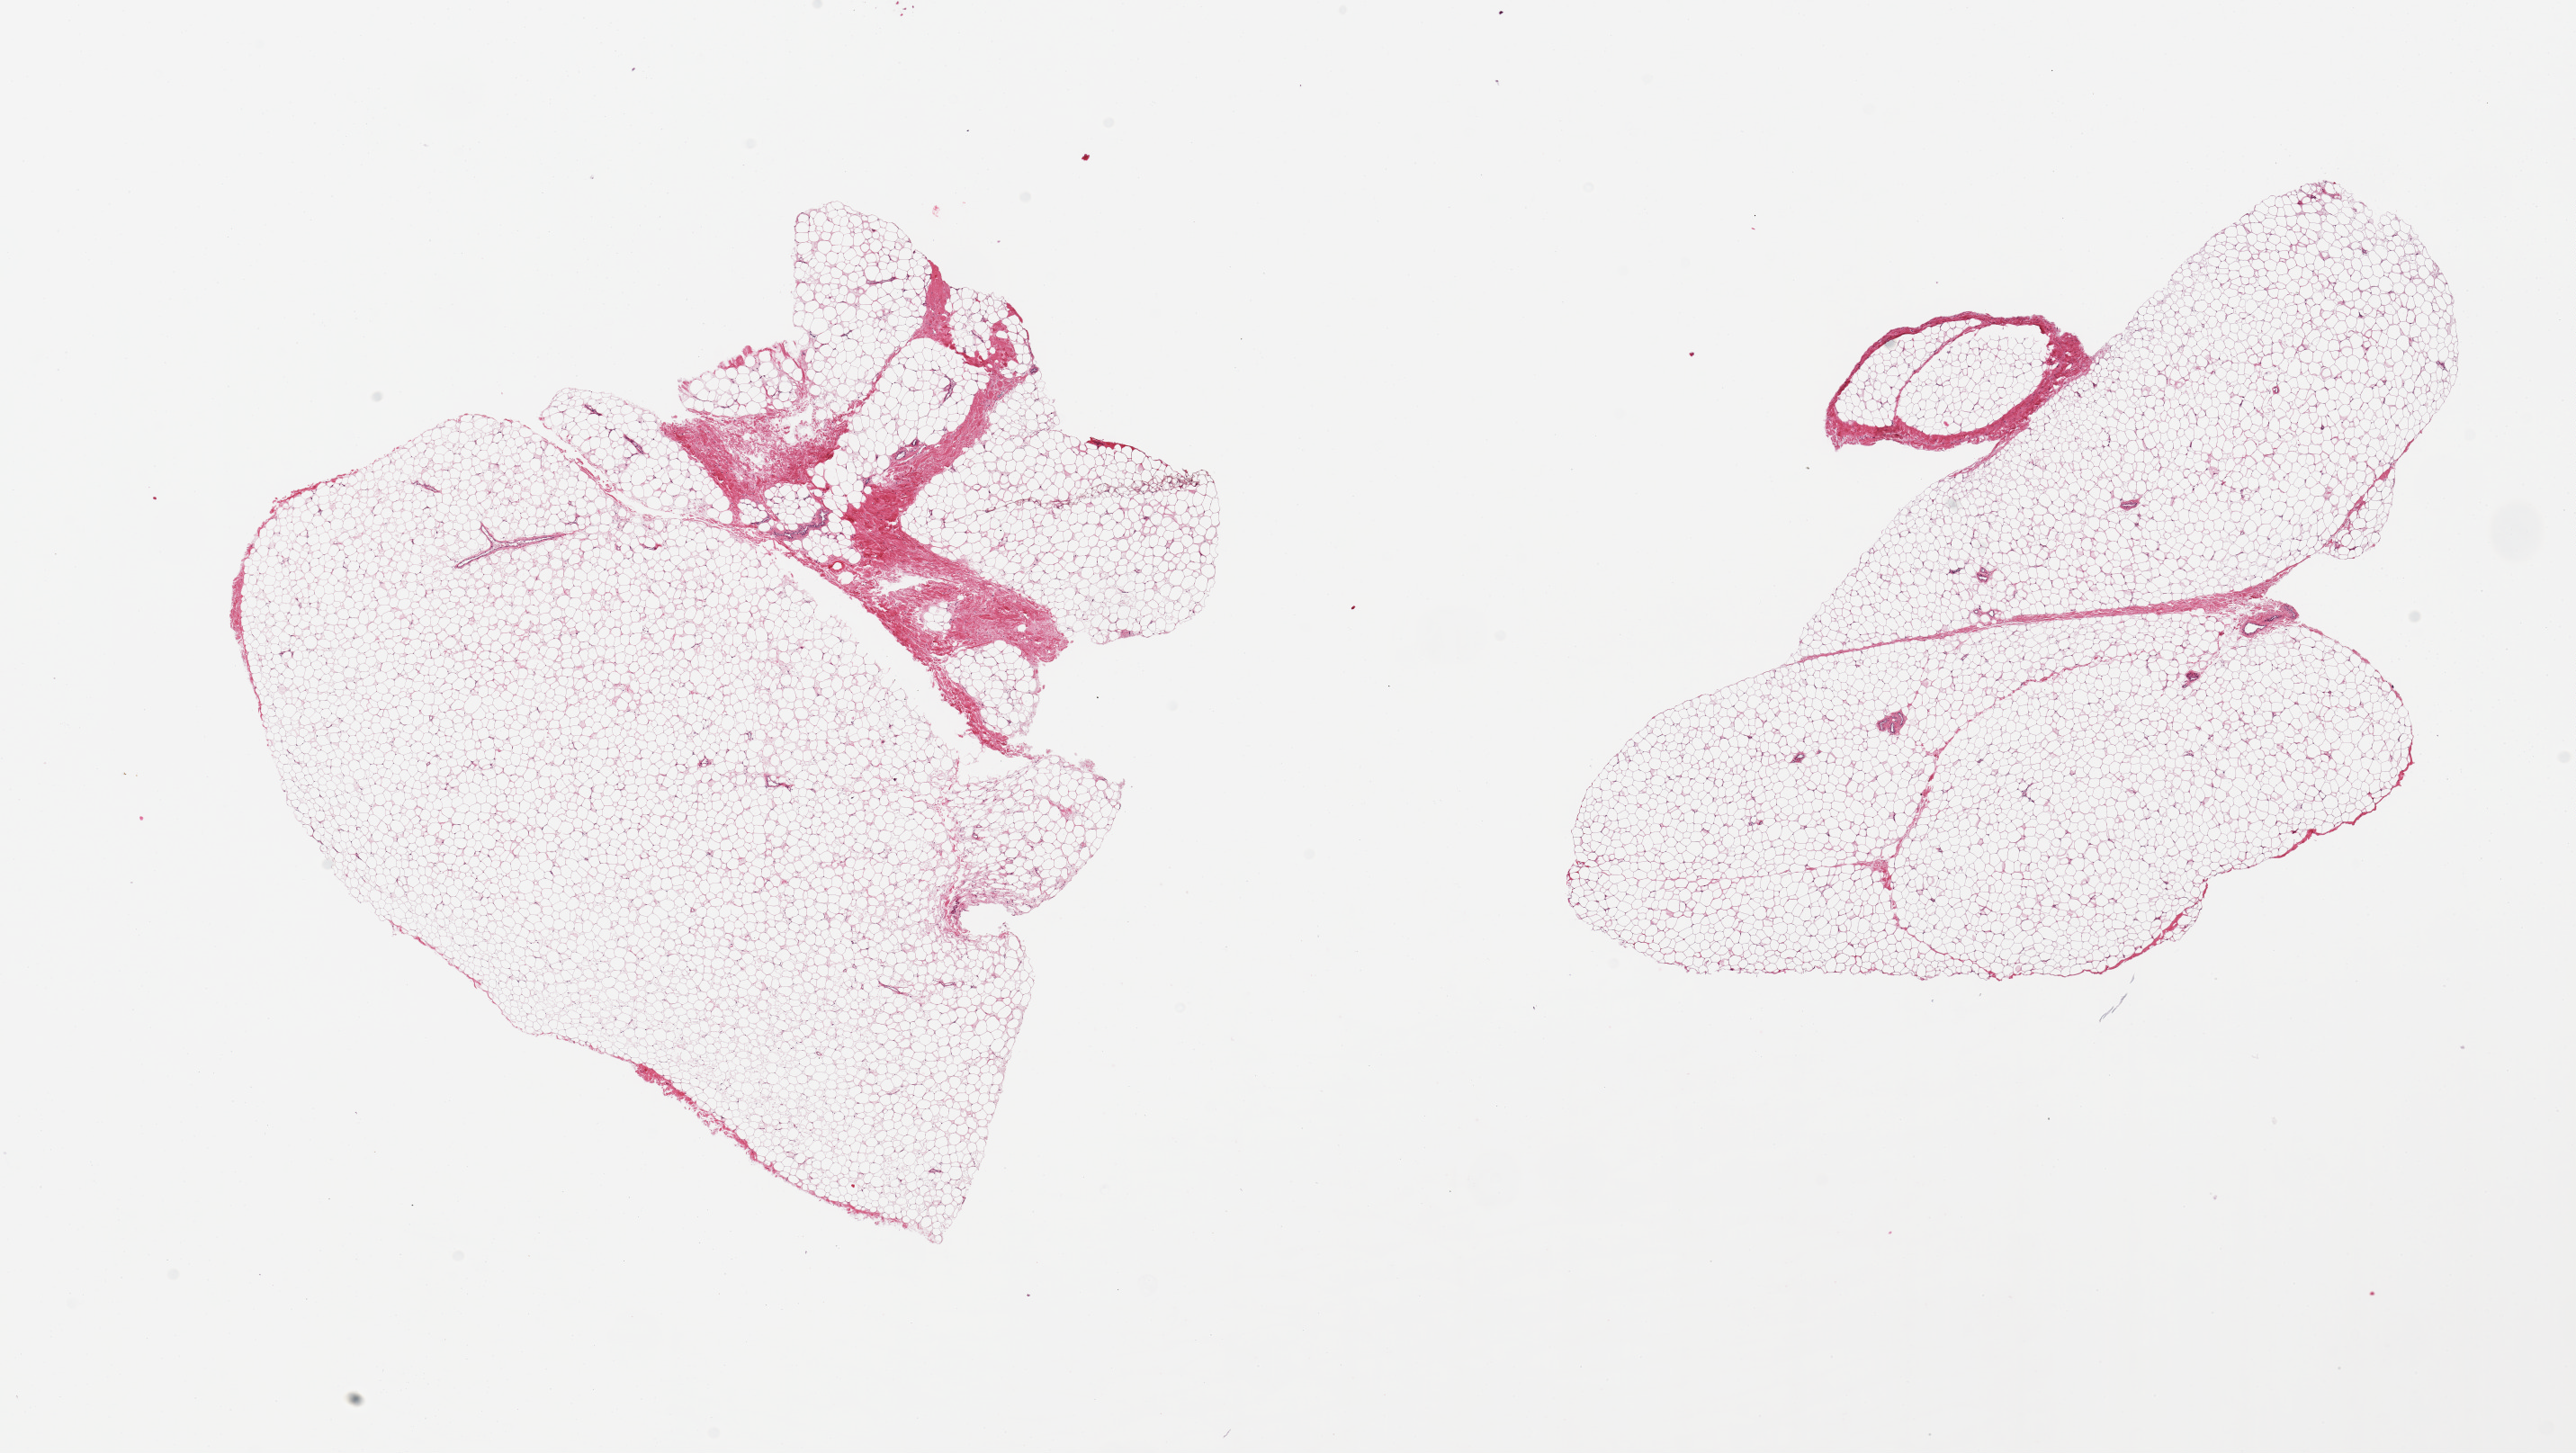
Whole-slide image, hematoxylin and eosin (H&E) stain — whole scanned area (about 22.6 x 12.8 mm) shown as a low-resolution overview, PAXgene-fixed paraffin-embedded (PFPE) section, target tissue: adipose tissue, tissue donor sample. Donor sex: female.
Reviewer comment on this tissue sample: 2 pieces, ~5% fascia/vasular elements.